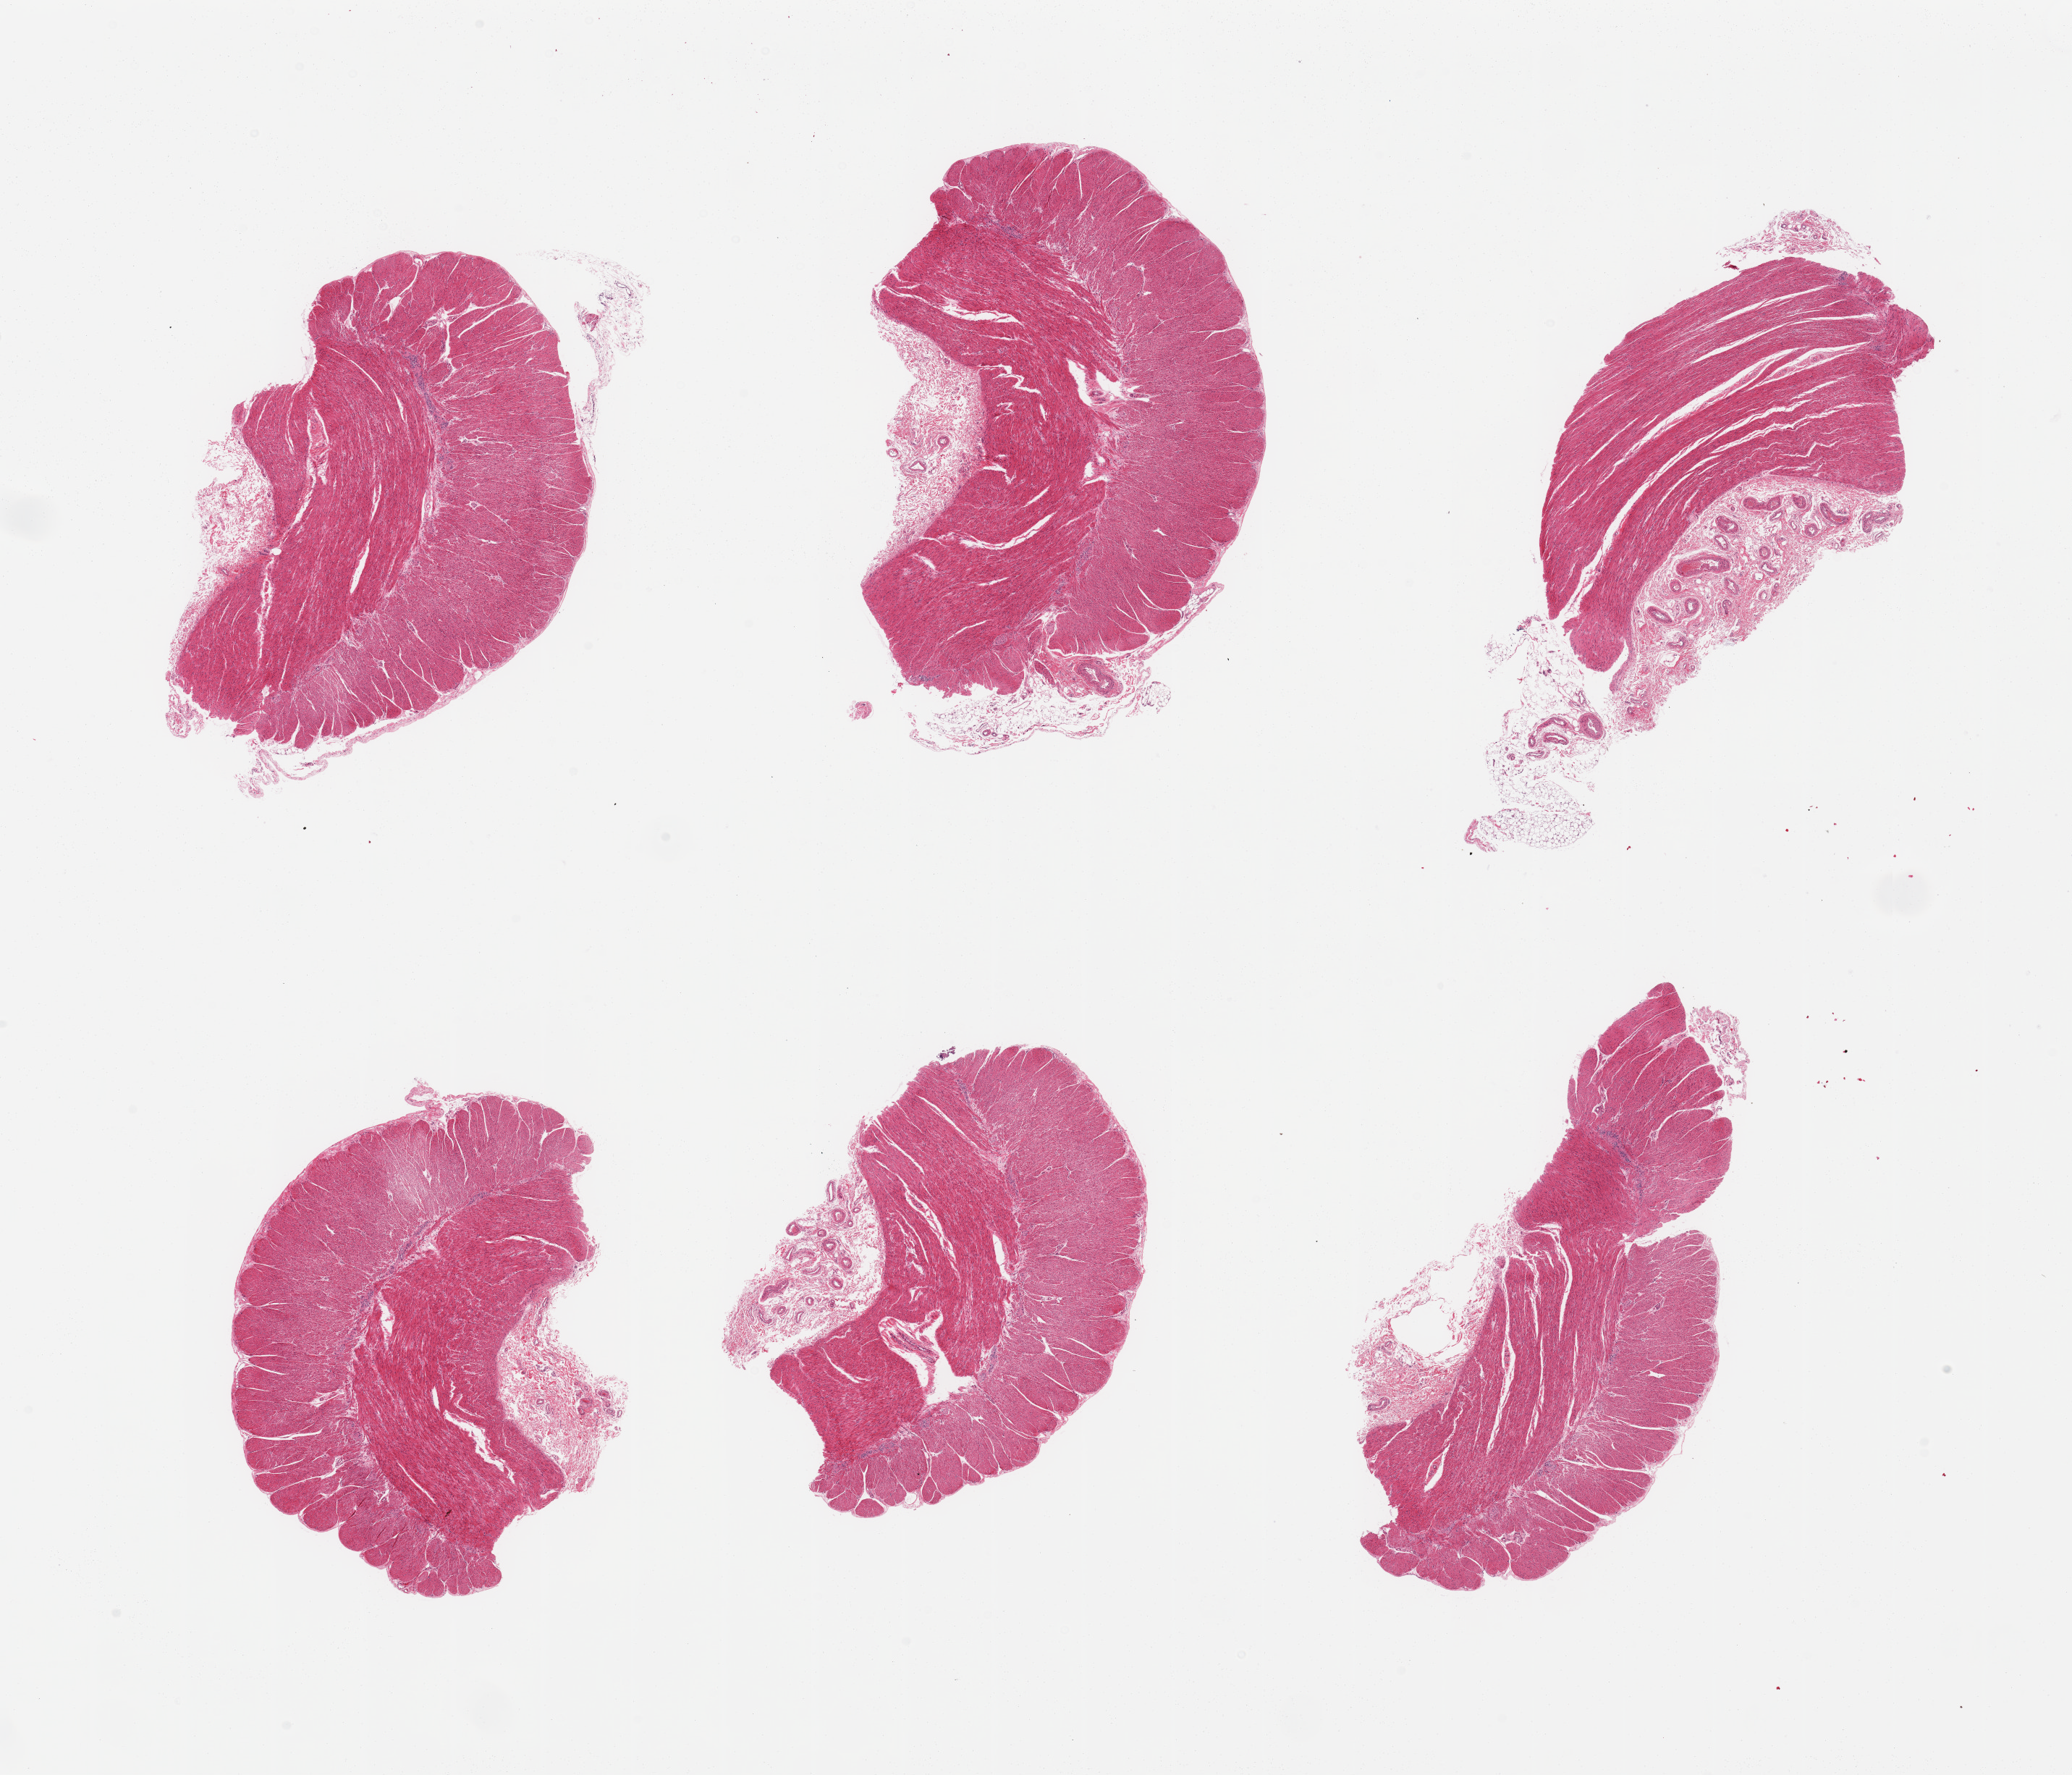
Whole-slide image, haematoxylin and eosin stain, shown as a low-resolution overview of the whole scanned area (about 22.6 x 19.4 mm). PAXgene-fixed paraffin-embedded (PFPE) section. Target tissue: sigmoid colon. Donor tissue sample. Donor sex: female.
Review note (as recorded): 6 pieces; well dissected muscularis with small amount of amount of submucosa.